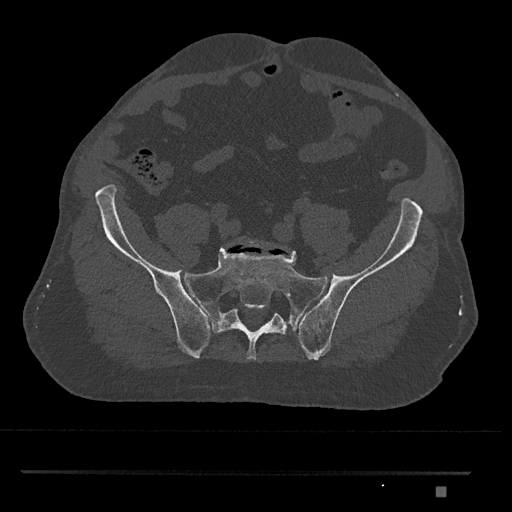
CT including the spine, one axial slice. Position 492 of 1134 along the scan axis. 120 kVp. Bone window (W 1800 / L 400 HU). 0.5 mm slice thickness. 512 × 512 image matrix, field of view 429 × 429 mm. Patient: male, 65 years. From the clinical record (not read from this slice): primary cancer: prostate.
Outlined on this slice (semi-automatic segmentation, software-assisted and operator-edited):
- L5 vertebra: bounding box [x1, y1, x2, y2] px = [241, 237, 278, 249]